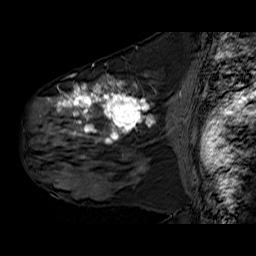
Breast MRI (dynamic contrast-enhanced), one sagittal slice; dynamic contrast-enhanced series, time point 2 of 6 at this slice position (early post-contrast); 1.5 T; TE 6.3 ms, TR 32.9 ms; 4 mm slice thickness; 256 × 256 image matrix, field of view 200 × 200 mm. Female patient. From the clinical record (not read from this slice): setting: breast cancer imaged before/during neoadjuvant chemotherapy; receptor status: HER2-positive.
Structures marked on this image (semi-automatically segmented with operator editing):
- analysis volume of interest (the breast-tissue region the enhancement analysis was run in; not a lesion): box from (x=30, y=78) to (x=175, y=180) px
- tumour enhancement mask (voxels above the 100 % enhancement threshold inside the analysis volume of interest): (x=49, y=79)–(x=154, y=170)